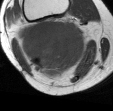
MRI of an extremity soft-tissue mass, one axial slice. Position 30 of 45 along the scan axis. MR volume resampled by the dataset authors to the PET/CT grid (not the native acquisition matrix). 113 × 111 image matrix. Female patient. From the clinical record (not read from this slice): histological type: liposarcoma; site of the primary tumour: right thigh.
Annotated regions visible in this slice (expert contour drawn on MRI and transferred to this co-registered scan by the dataset authors):
- gross tumour volume (mass): bounding box [x1, y1, x2, y2] px = [17, 19, 88, 79]